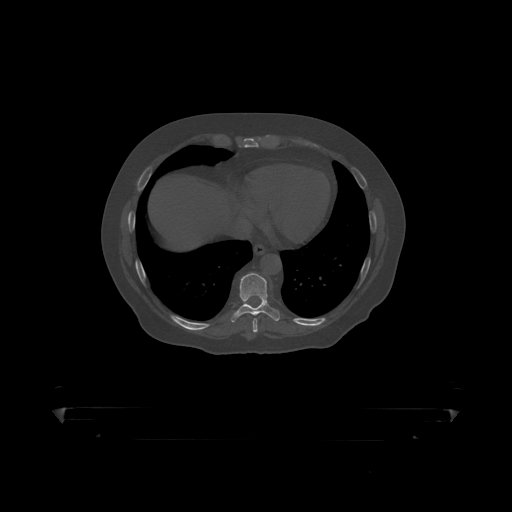
CT including the spine, one axial slice; position 239 of 390 along the scan axis; bone window (W 1800 / L 400 HU); 512 × 512 image matrix, field of view 650 × 650 mm. Male patient, age 60 years. Case-level facts recorded for this patient, not image findings: primary cancer: prostate.
Annotated regions visible in this slice (semi-automatic segmentation, software-assisted and operator-edited):
- T9 vertebra: bounding box [x1, y1, x2, y2] px = [233, 273, 281, 317]